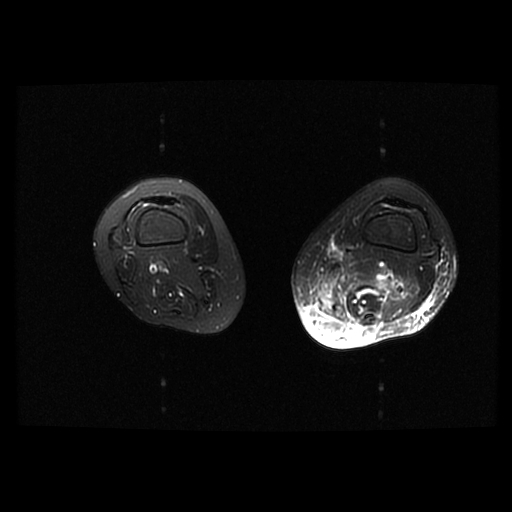
MRI of an extremity soft-tissue mass, one axial slice. Position 15 of 42 along the scan axis. T2-weighted fat-saturated. 6 mm slice thickness. 512 × 512 image matrix, field of view 420 × 420 mm. Female patient. From the clinical record (not read from this slice): histological type: pleomorphic leiomyosarcoma; grade: high; site of the primary tumour: left thigh.
Annotated regions visible in this slice (outlined manually by an expert reader):
- gross tumour volume including surrounding oedema: bounding box (x1, y1, x2, y2) in pixels: (317, 259, 392, 318)